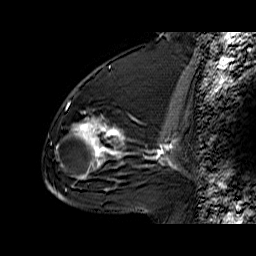
Breast MRI (dynamic contrast-enhanced), one sagittal slice. Position 35 of 60 along the scan axis. Dynamic contrast-enhanced series, time point 2 of 6 at this slice position (early post-contrast). 1.5 T. TE 6.3 ms, TR 32.9 ms. 256 × 256 image matrix. Female patient. Case-level facts recorded for this patient, not image findings: setting: breast cancer imaged before/during neoadjuvant chemotherapy; receptor status: triple-negative.
Annotated regions visible in this slice (semi-automatic segmentation, software-assisted and operator-edited):
- analysis volume of interest (the breast-tissue region the enhancement analysis was run in; not a lesion): bounding box <55,76,129,170> (left, top, right, bottom; pixels)
- tumour enhancement mask (voxels above the 100 % enhancement threshold inside the analysis volume of interest): <72,118,125,167>